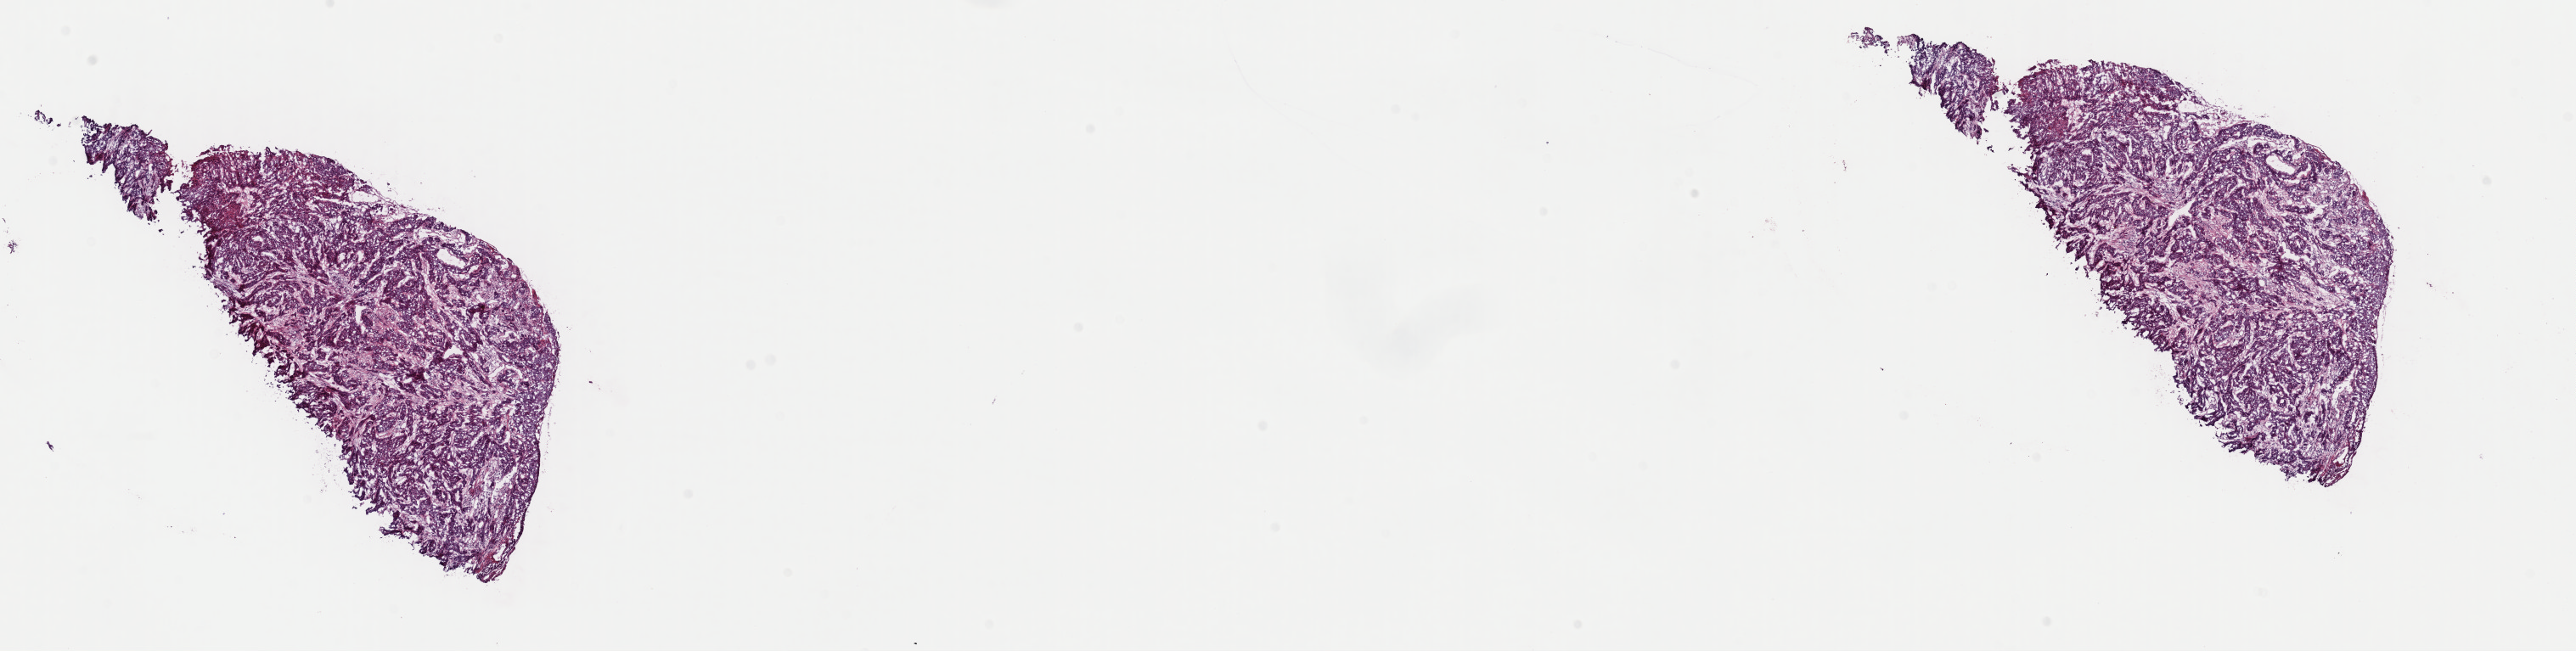
Digitized H&E tissue section (whole slide), low-resolution overview of the scanned area, about 24.0 x 6.1 mm. Frozen section from the top of the tissue portion. Primary tumour sample from the cervix. Female, age 55 years at initial diagnosis. Histologic grade: GX (grade cannot be assessed). Slide review estimates, as recorded: tumour cells 80%, tumour nuclei 80%, normal cells 0%, stromal cells 20%, necrosis 0%. Infiltration values recorded for this section: lymphocyte infiltration 0%, monocyte infiltration 0%, neutrophil infiltration 0%.
Histologic diagnosis: Squamous cell carcinoma, large cell, nonkeratinizing, NOS (cervix uteri). FIGO stage: I.